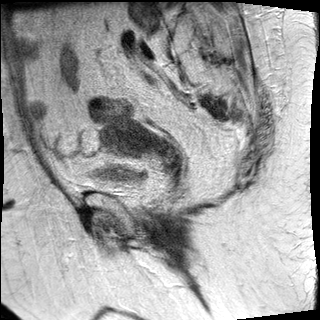
Pelvic MRI for cervical cancer, one sagittal slice. T2-weighted. 1.5 T. TE 89 ms, TR 2740 ms. 4 mm slice thickness. 320 × 320 image matrix, field of view 260 × 260 mm. Patient: female, 67 years.
Outlined on this slice (outlined manually by an expert reader):
- uterus and cervix: bounding box <100,116,179,160> (left, top, right, bottom; pixels)